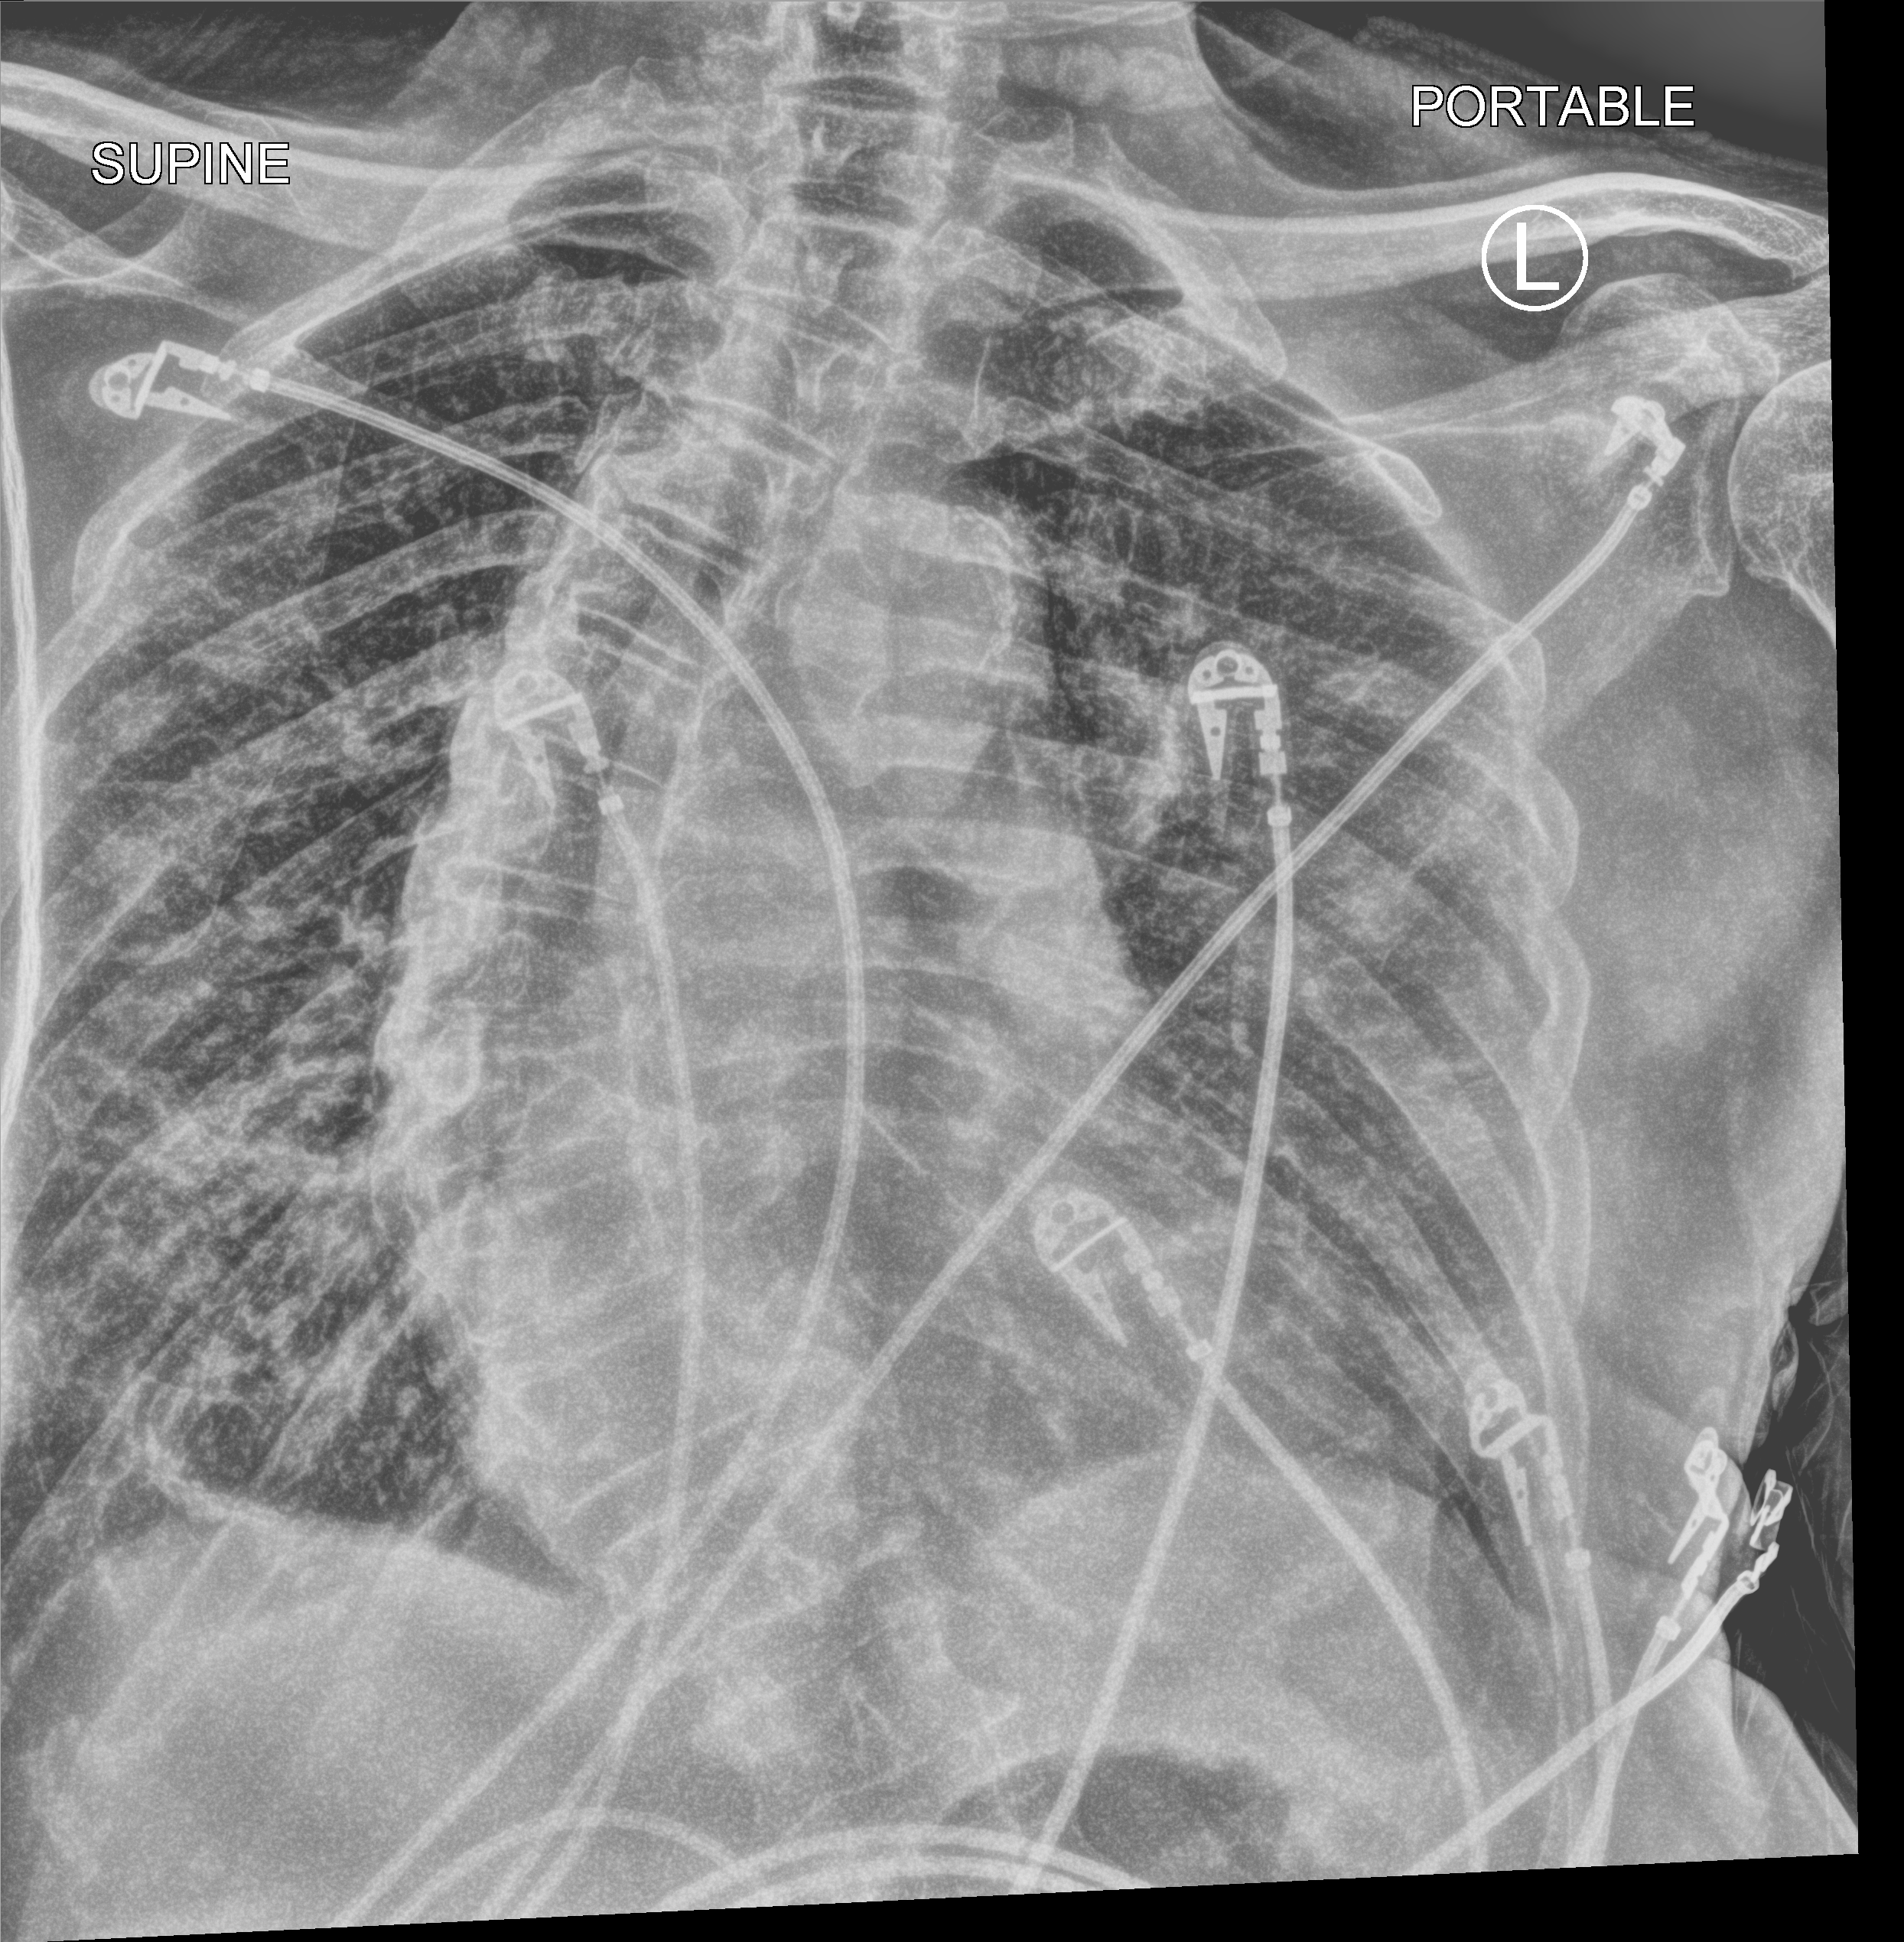
Portable chest radiograph, anteroposterior (AP) projection. Male patient hospitalised with COVID-19, age 75–90 years.
From the hospital-stay record, not from the radiograph (when in the stay this image was taken is not recorded): length of hospital stay: 12 days; mechanically ventilated during this hospital stay: no; admitted to intensive care during this hospital stay: no.